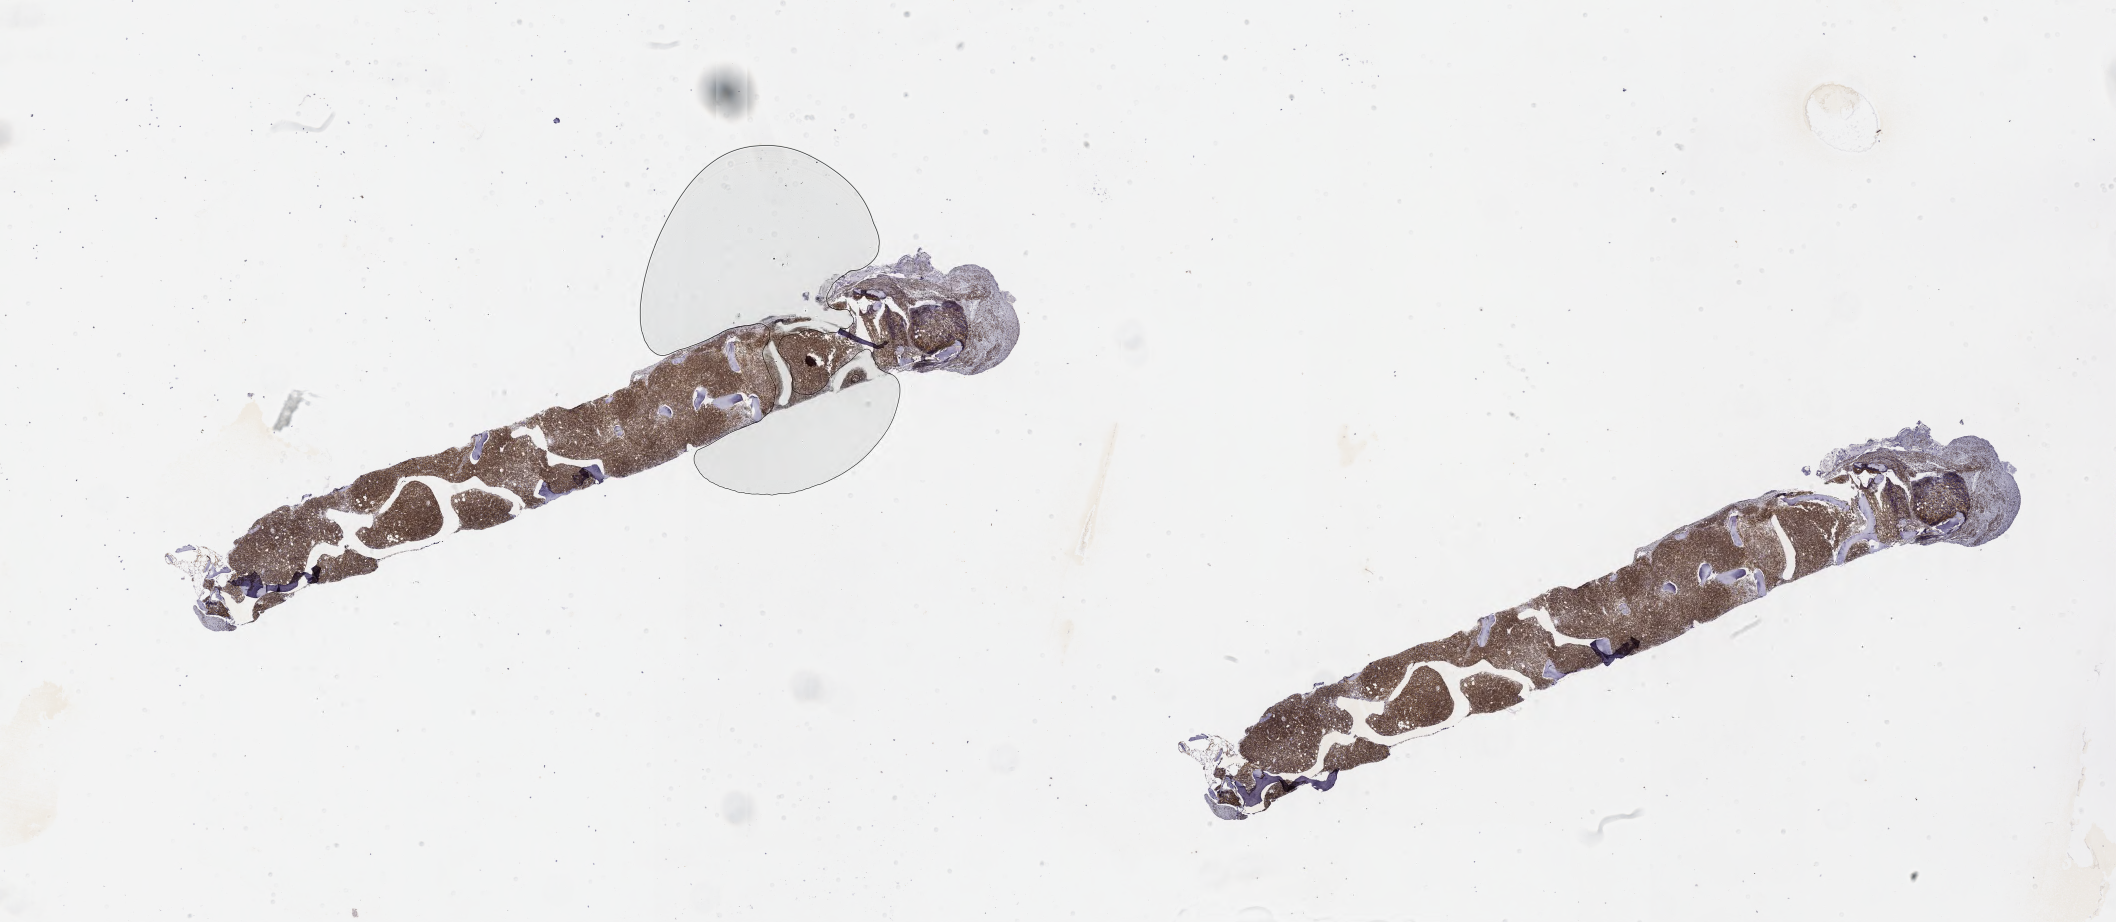
IHC for CD10, whole-slide image, a low-resolution overview of the entire scanned area, about 34.2 x 14.9 mm, tumor tissue. Patient: female, age 64 years.
Histologic diagnosis: Burkitt lymphoma, NOS.